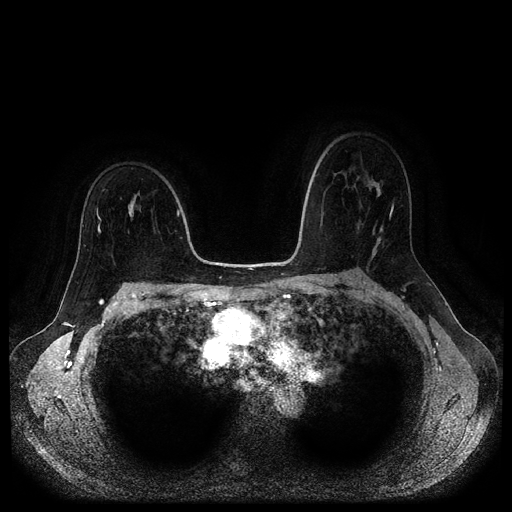
Breast MRI (dynamic contrast-enhanced, multi-phase), one axial slice; slice 67 of 116 in the series (ordered by position); dynamic contrast-enhanced series, time point 2 of 5 at this slice position (early post-contrast); 1.5 T; TE 2.6 ms, TR 5.3 ms; 2 mm slice thickness; 512 × 512 image matrix, field of view 360 × 360 mm. Female patient, age 50 years.
Annotated regions visible in this slice (semi-automatically segmented with operator editing):
- breast lesion (labelled benign in the annotation): bounding box [x1, y1, x2, y2] px = [127, 192, 139, 221]